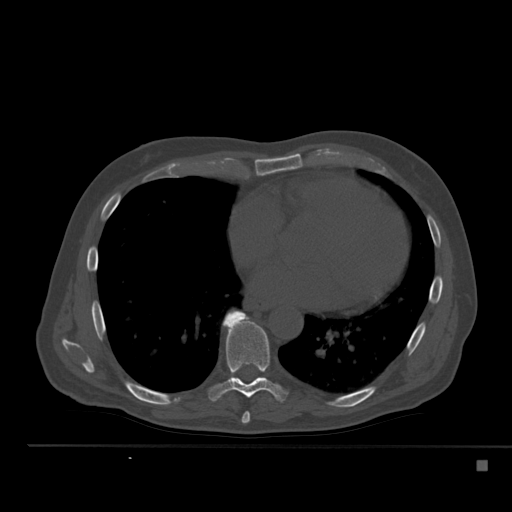
CT including the spine, one axial slice; slice 308 of 517 in the series (ordered by position); reconstruction kernel Br40s; 120 kVp; bone window (W 1800 / L 400 HU); 1.5 mm slice thickness; 512 × 512 image matrix, field of view 408 × 408 mm. Male patient, age 70 years. Case-level facts recorded for this patient, not image findings: primary cancer: renal.
Annotated regions visible in this slice (semi-automatic segmentation, software-assisted and operator-edited):
- T7 vertebra: bounding box (x1, y1, x2, y2) in pixels: (241, 412, 250, 424)
- T8 vertebra: (209, 310, 286, 402)